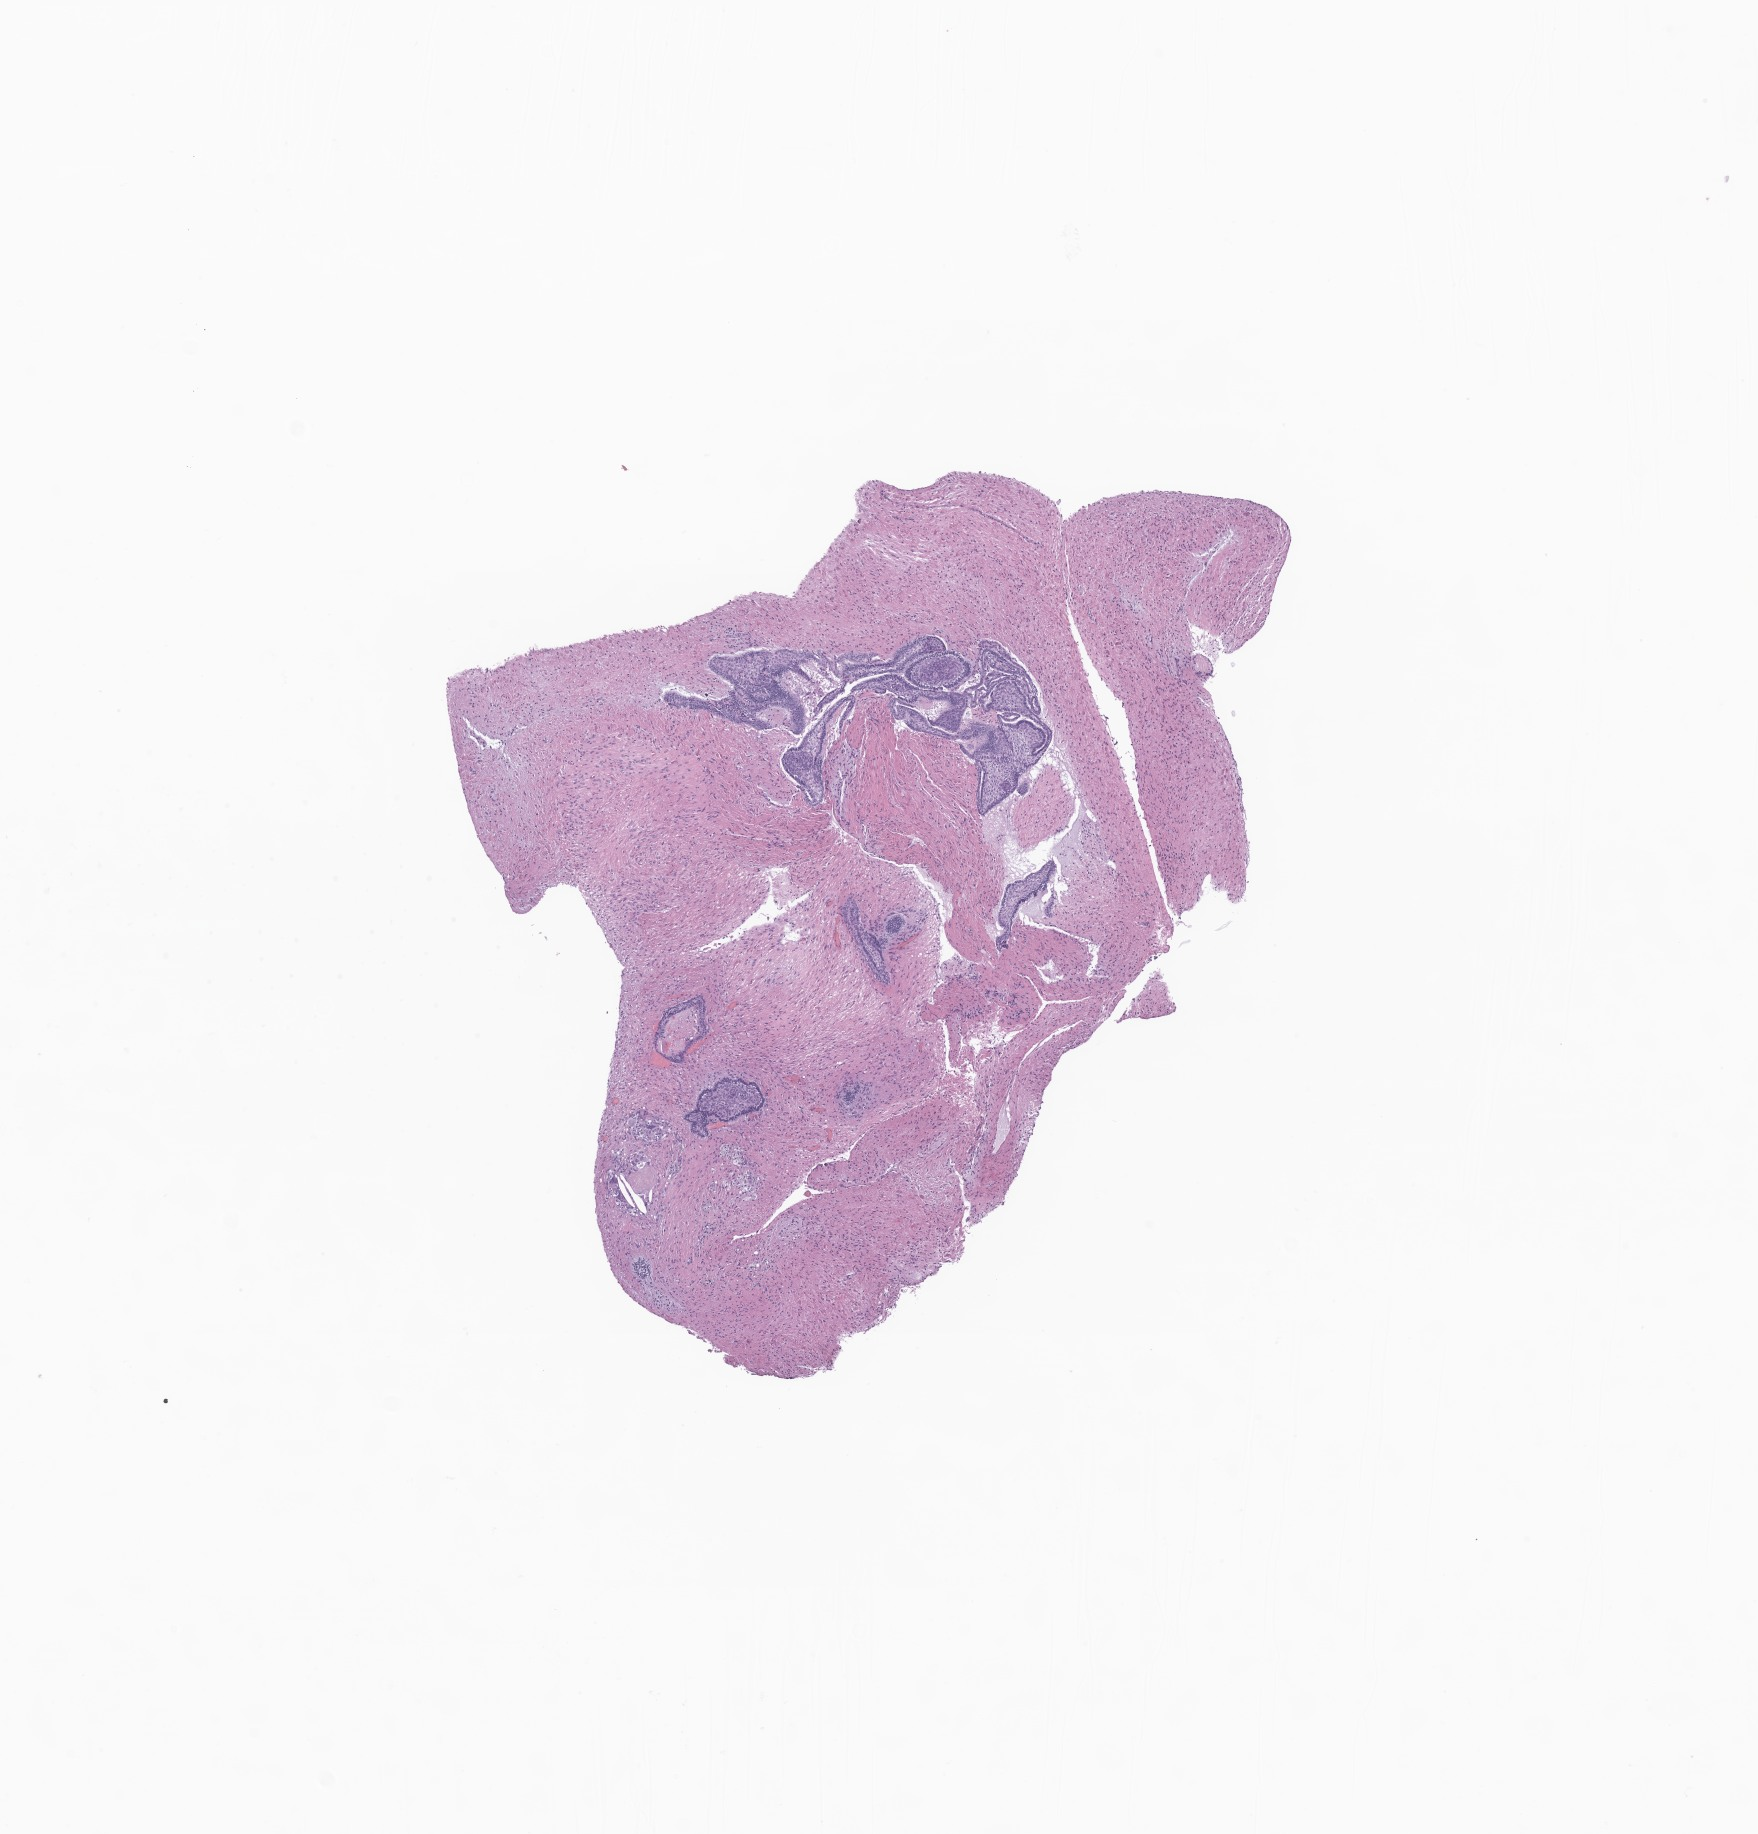
H&E whole-slide image of tumor tissue from the brain — a low-resolution overview of the entire scanned area, about 7.4 x 7.7 mm, FFPE section. Patient female; age 130 months (10 years 10 months).
Diagnosis (ICD-O-3 morphology term): Neoplasm, uncertain whether benign or malignant.